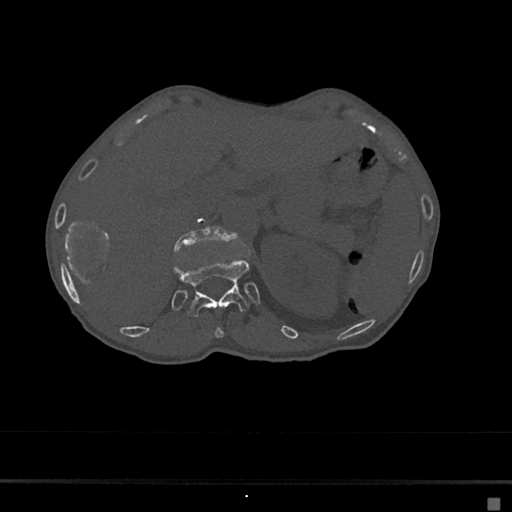
CT including the spine, one axial slice. Position 121 of 797 along the scan axis. 120 kVp. Bone window (W 1800 / L 400 HU). 0.5 mm slice thickness. 512 × 512 image matrix. Female patient, age 68 years. From the clinical record (not read from this slice): primary cancer: renal.
Outlined on this slice (semi-automatically segmented with operator editing):
- L1 vertebra: bounding box [x1, y1, x2, y2] px = [174, 225, 236, 251]
- T11 vertebra: [214, 327, 224, 339]
- T12 vertebra: [173, 257, 250, 319]